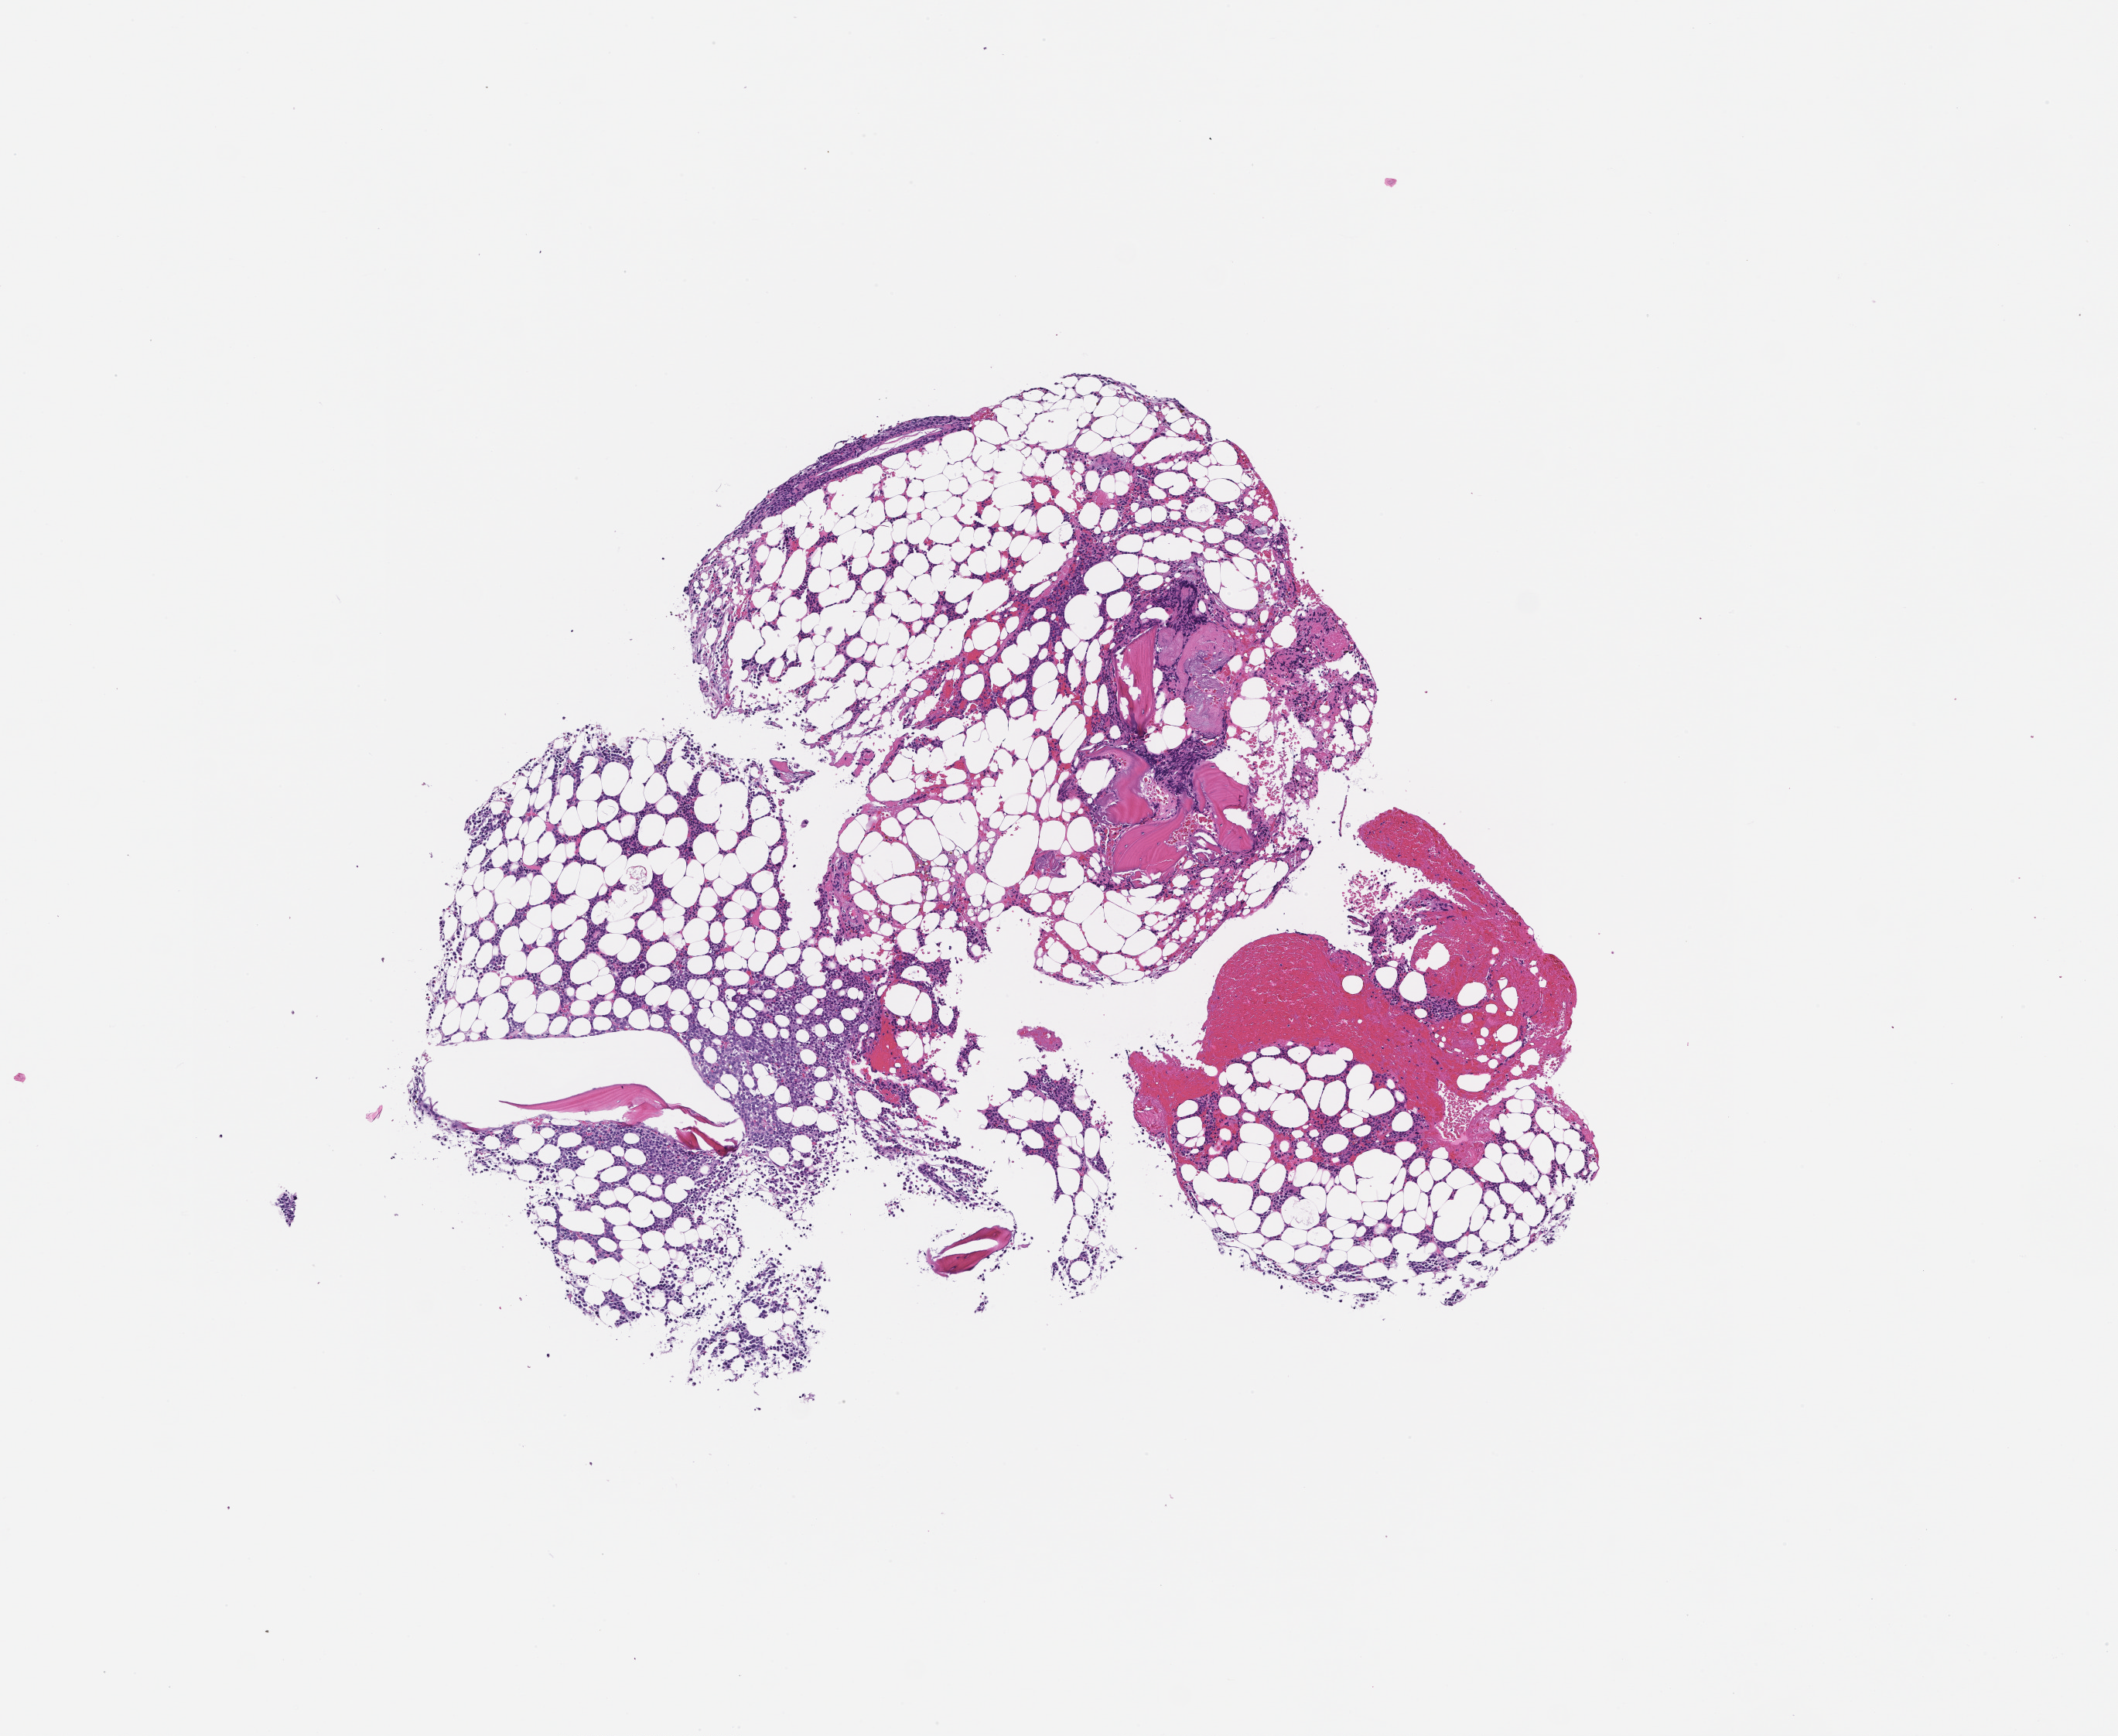
Digitized H&E-stained section, a low-resolution overview of the entire scanned area, about 5.5 x 4.5 mm; formalin-fixed paraffin-embedded section; specimen time point: collected at baseline (before treatment). Patient sex: male.
- this section: metastasis (sampled organ not recorded)
- patient diagnosis (primary): Plasma Cell Myeloma